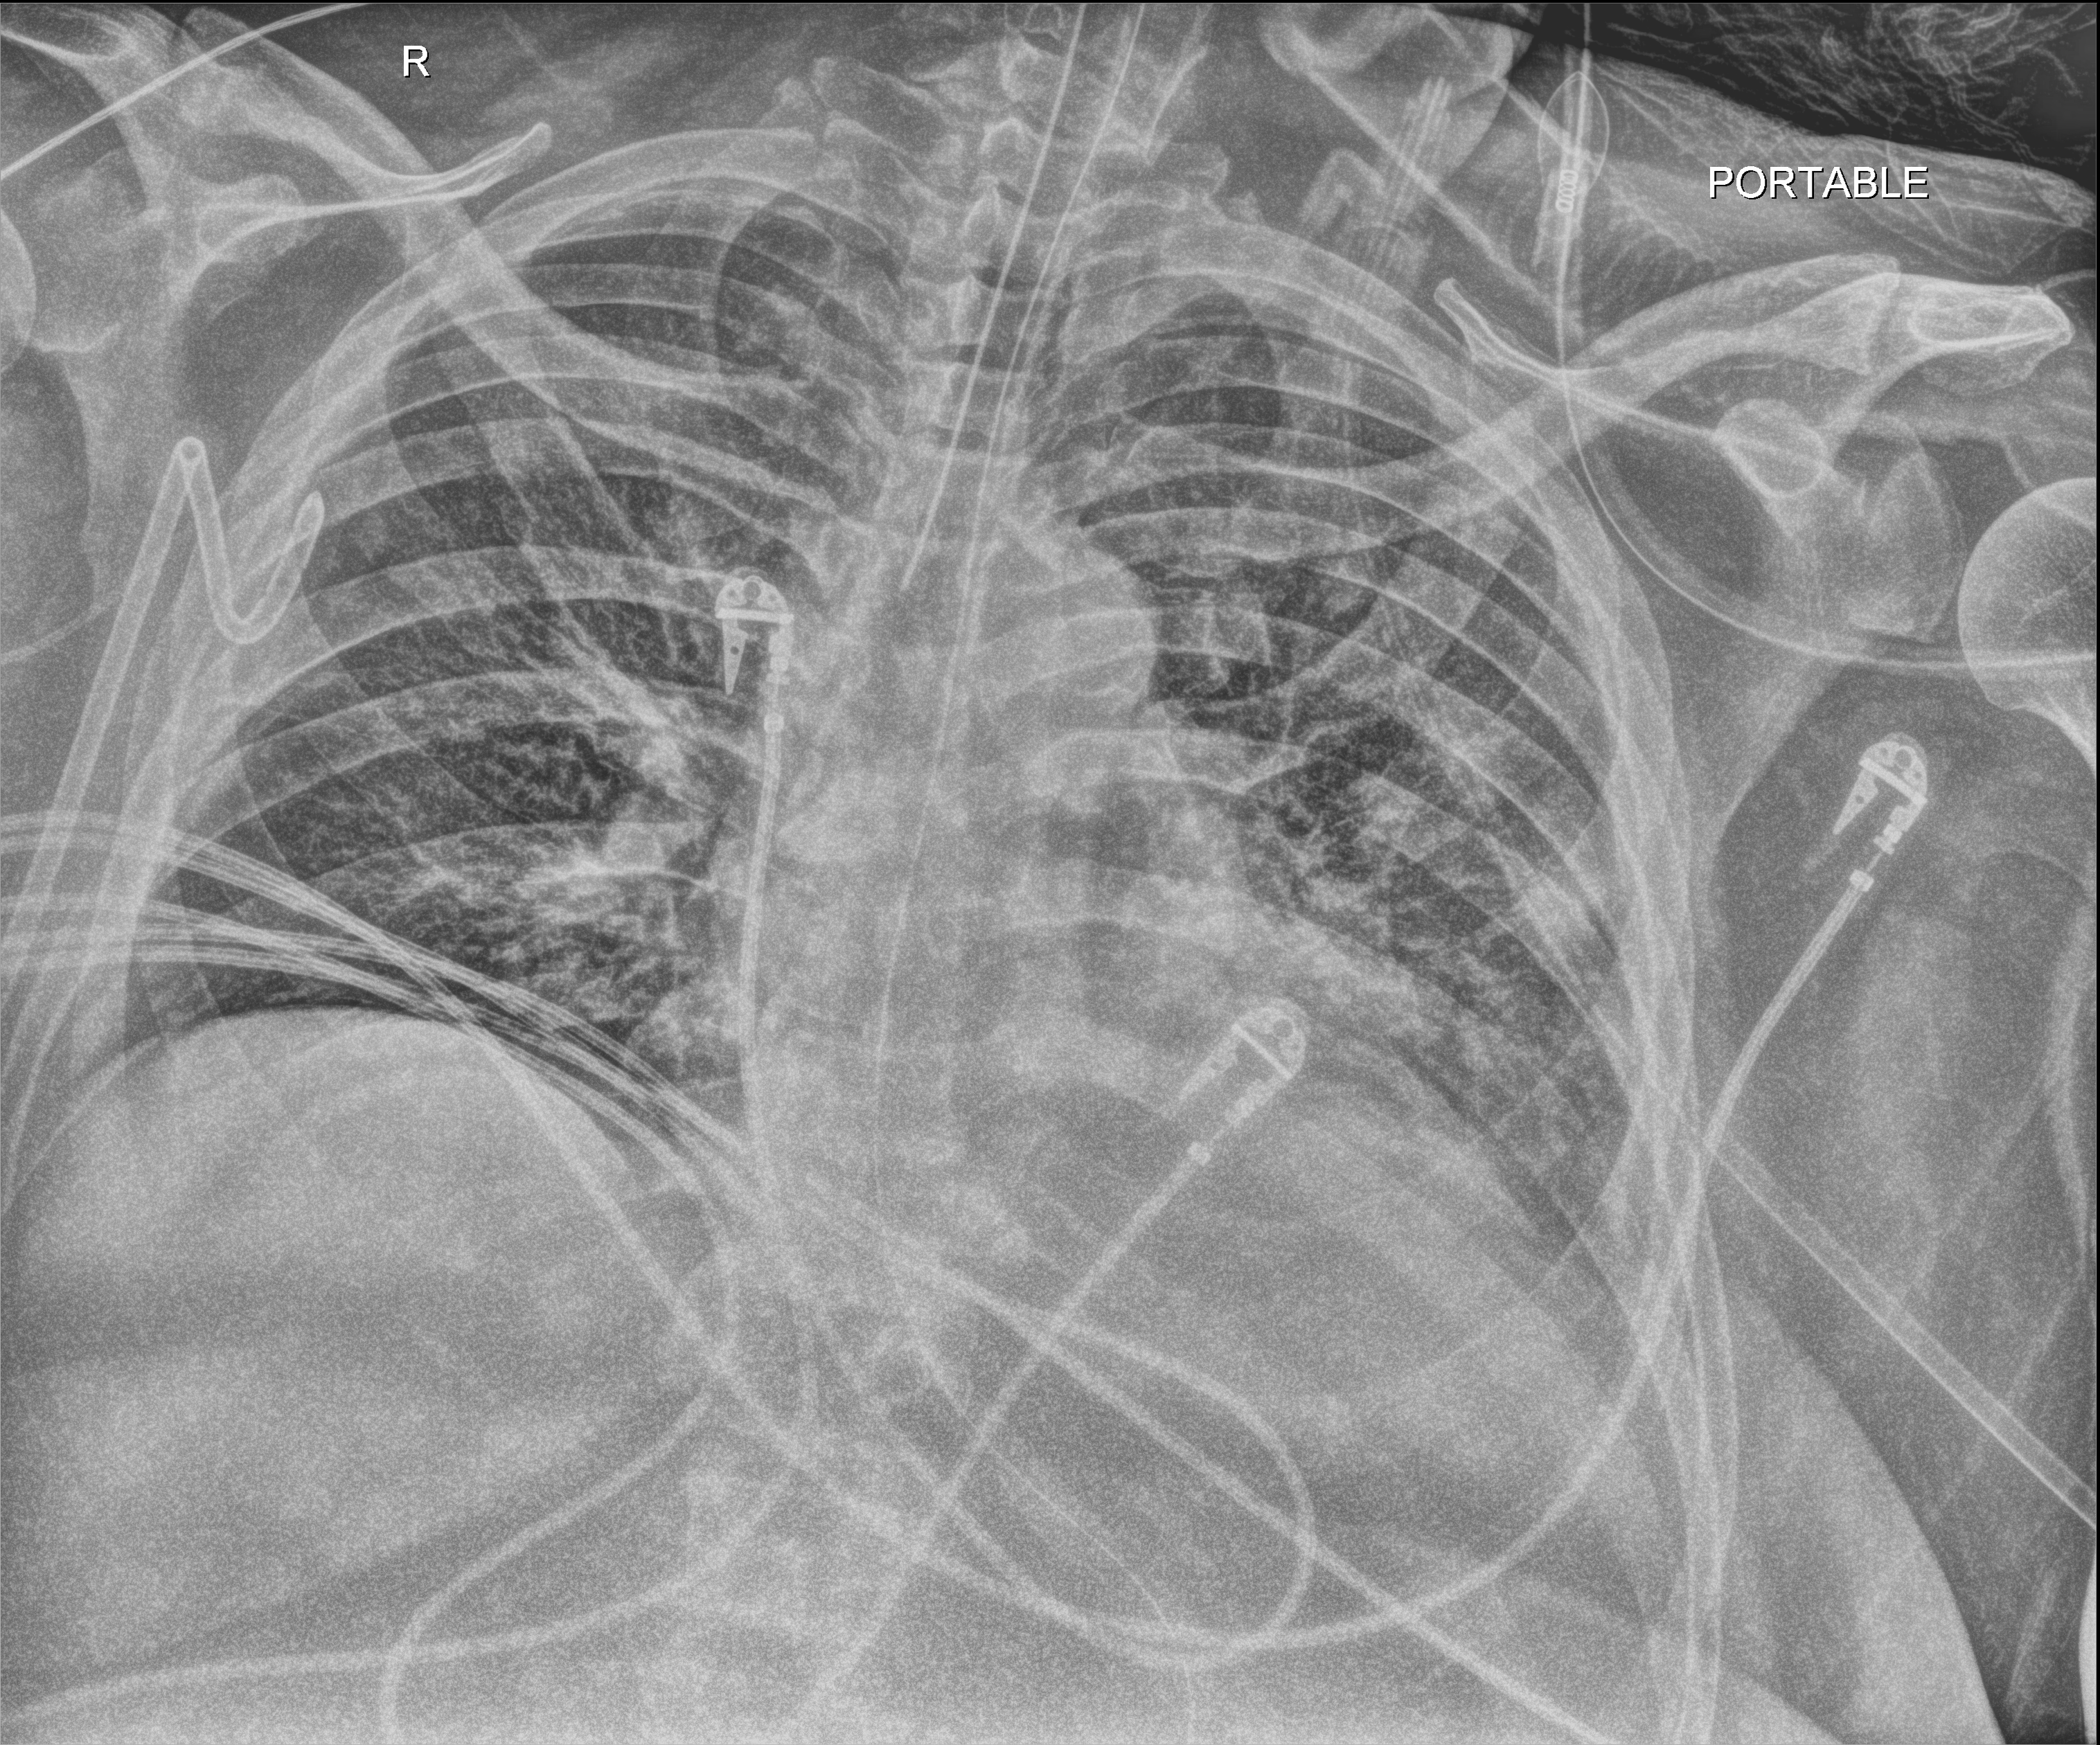
Chest X-ray (portable), anteroposterior (AP) projection. Patient hospitalised with COVID-19; male, aged 60–74 years.
Hospital-stay facts (about this admission, not read from this image; timing relative to this image not recorded): mechanically ventilated during this hospital stay: yes; hypertension (admission record): yes; admitted to intensive care during this hospital stay: yes.